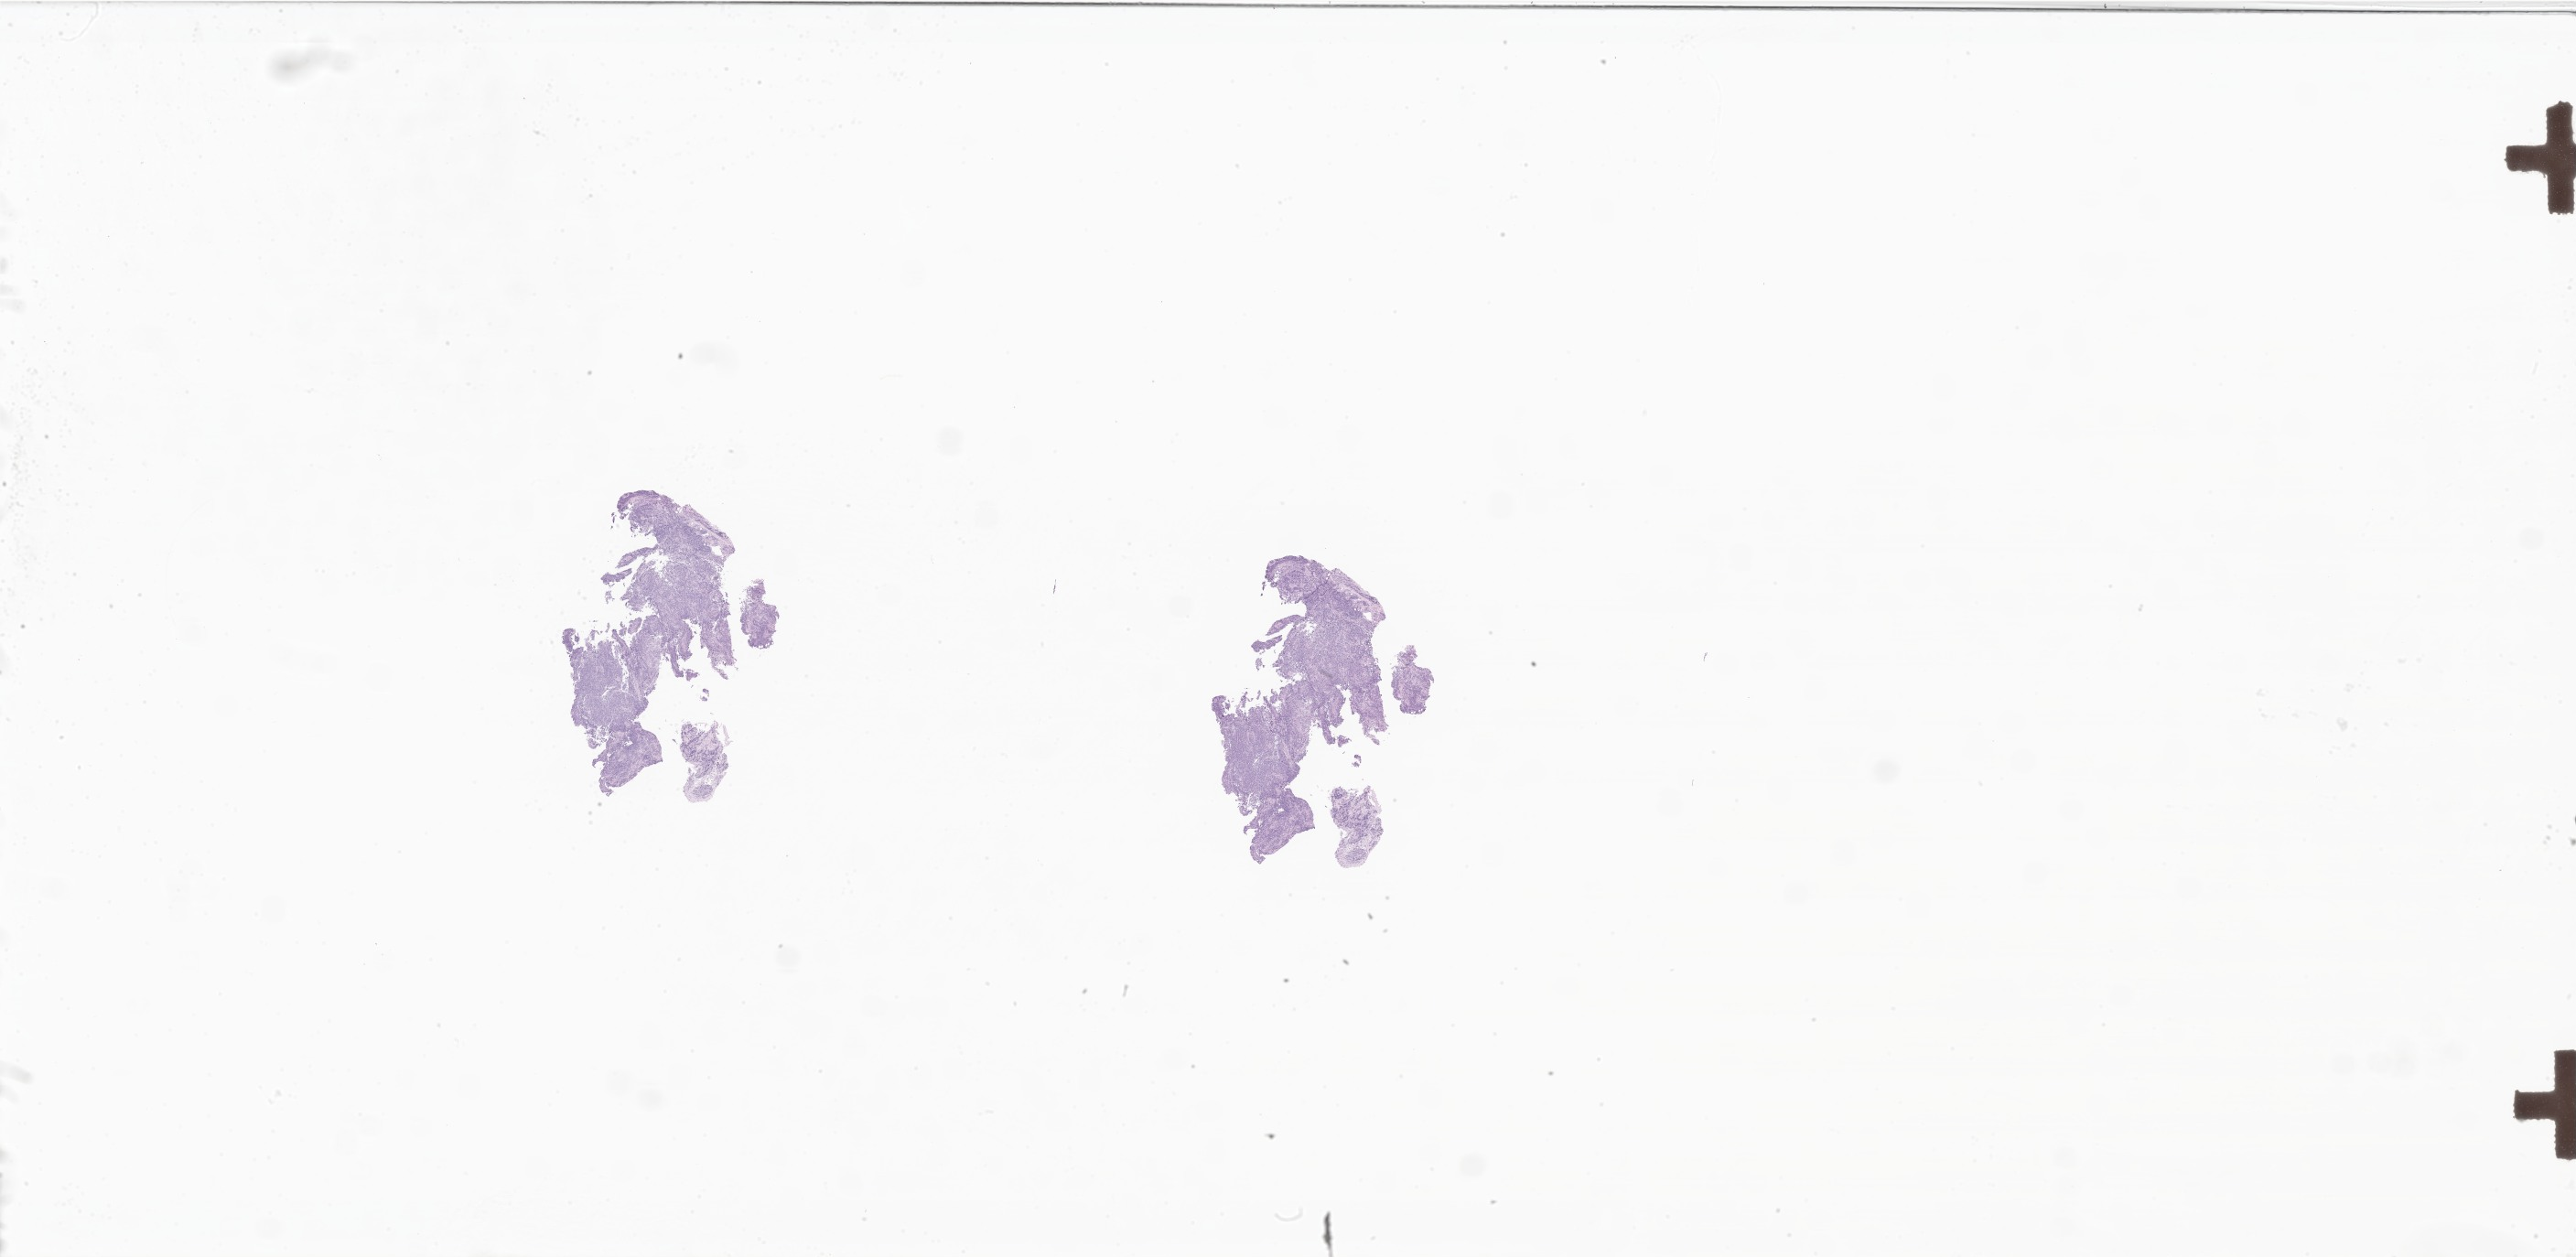
Haematoxylin and eosin whole-slide image of tumor tissue from the upper limb — low-resolution overview of the scanned area, about 47.5 x 23.2 mm. Formalin-fixed, paraffin-embedded (FFPE) tissue. Female patient, age 65 months (5 years 5 months).
- diagnosis (ICD-O-3 morphology term): Alveolar rhabdomyosarcoma